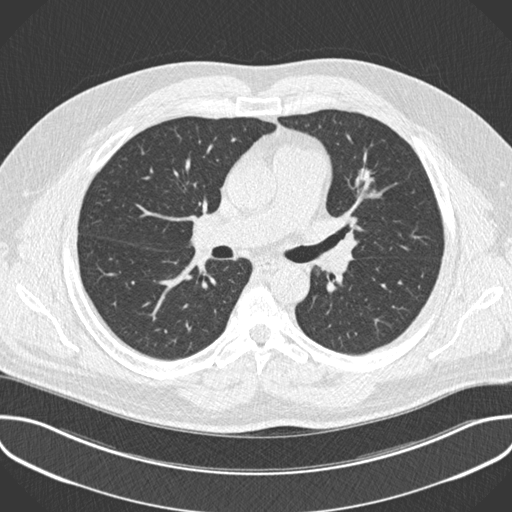
Chest CT (low-dose screening protocol), one axial image. Baseline screening round. Lung window (W 1500 / L -600 HU). 2 mm slice thickness. Standard (soft-tissue) reconstruction kernel (B30f). Slice 75 of 201 in the series. Male, age 55 years at enrolment. Former smoker at enrolment.
Lesion marked by an expert reader, box from (x=345, y=159) to (x=391, y=194) px. Screening reader's record for this exam (one nodule recorded; not confirmed to be the boxed lesion): non-calcified nodule or mass ≥4 mm, lingula, 13 × 12 mm, spiculated (stellate) margins, soft tissue attenuation. Official screen result: positive, change unspecified: nodule(s) >= 4 mm or enlarging nodule(s), mass(es), or other non-specific abnormalities suspicious for lung cancer. Lung cancer was diagnosed 169 days after this screen: adenocarcinoma, NOS, left upper lobe, stage IA (AJCC 6th edition), 13 mm at pathology.